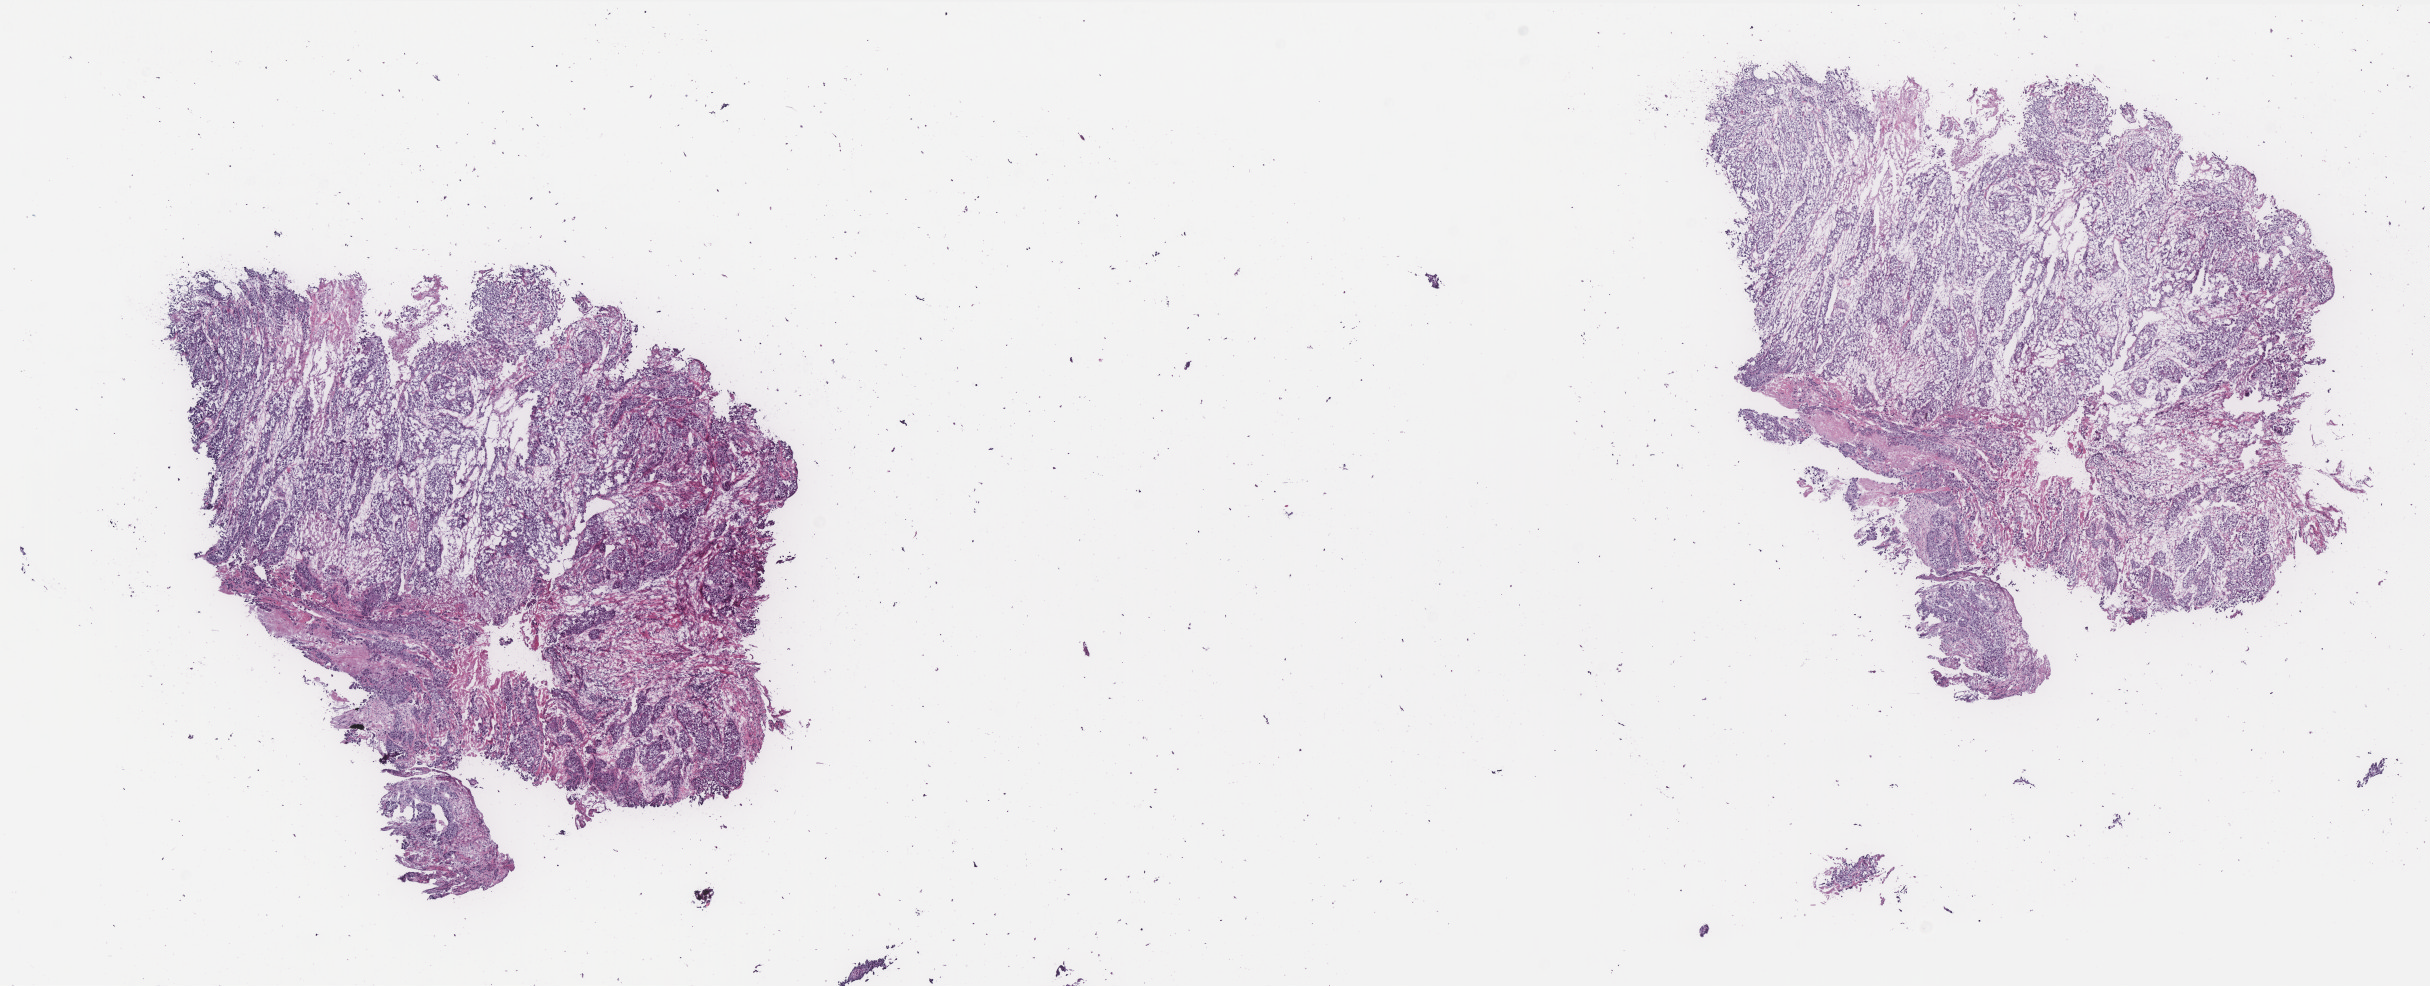
Digitized H&E tissue section (whole slide) — low-resolution overview of the scanned area, about 19.5 x 7.9 mm (from a 40x scan); frozen section from the top of the tissue portion; primary tumour sample from the cervix. Female patient; age at initial diagnosis 42 years. Histologic grade: G2 (moderately differentiated). Composition of this section per pathologist review: tumour cells 85%, tumour nuclei 85%, normal cells 0%, stromal cells 10%, necrosis 5%. Inflammatory infiltration, as recorded: lymphocyte infiltration 40%, monocyte infiltration 20%, neutrophil infiltration 20%.
* FIGO stage: IIIB
* pathologic diagnosis: Squamous cell carcinoma, NOS (cervix uteri)